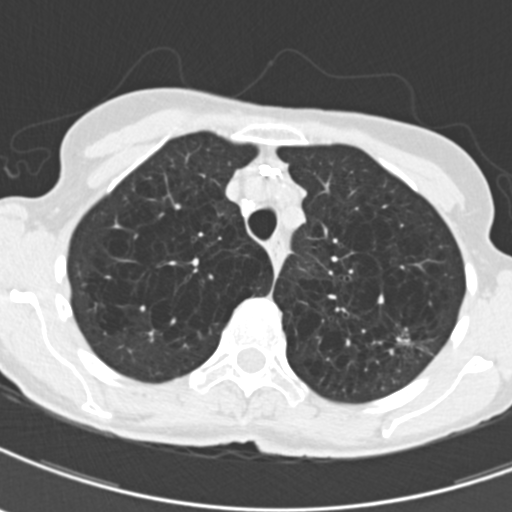
Low-dose screening chest CT, one axial slice. Reconstruction kernel B30f. Lung window (W 1500 / L -600 HU). 2 mm slice thickness. 512 × 512 image matrix.
Annotated regions visible in this slice (expert manual segmentation):
- lesion 1 (tumor, upper lobe of left lung): bounding box <397,338,414,346> (left, top, right, bottom; pixels)